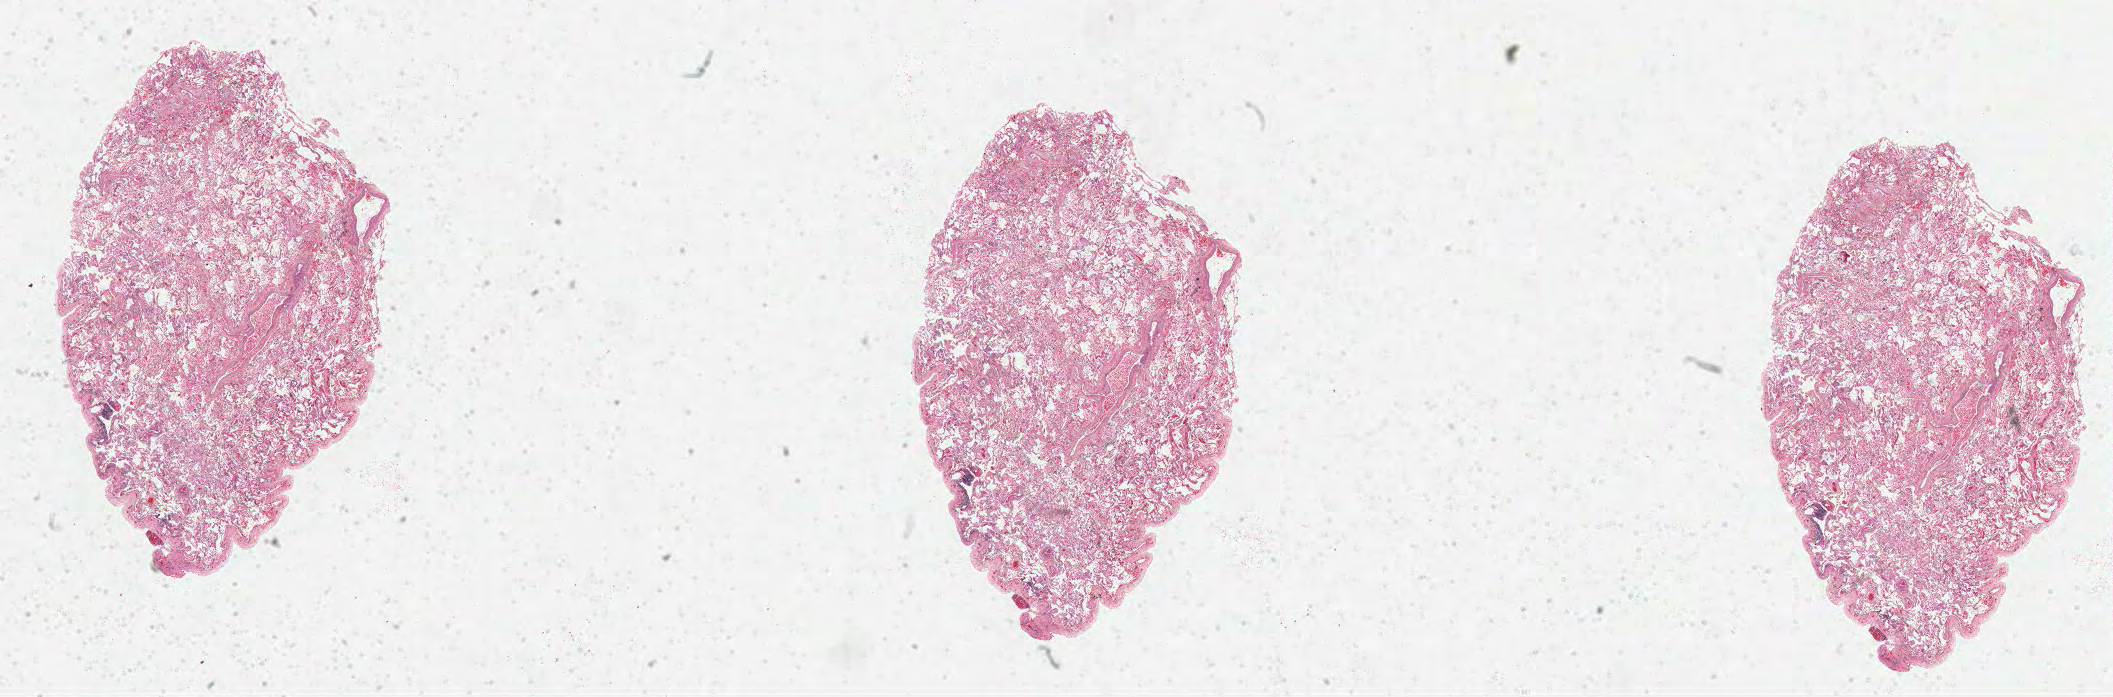
Whole-slide histology image, H&E-stained, a low-resolution overview of the entire scanned area, about 34.1 x 11.2 mm (acquisition: 40x scan), formalin-fixed paraffin-embedded (FFPE) diagnostic section, primary tumour sample from the lung. Female patient; age at initial diagnosis 72 years.
Pathologic diagnosis: Adenocarcinoma, NOS.